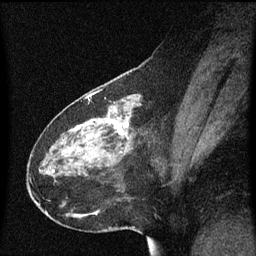
Breast MRI (dynamic contrast-enhanced), one sagittal slice; position 25 of 60 along the scan axis; dynamic contrast-enhanced series, image 2 of 3 at this slice position (ordered by acquisition); 1.5 T; TE 4.2 ms, TR 8.4 ms; 2 mm slice thickness; 256 × 256 image matrix. Patient: female, 49 years. From the clinical record (not read from this slice): setting: breast cancer imaged before/during neoadjuvant chemotherapy; receptor status: HR-positive, HER2-negative.
Structures marked on this image (semi-automatically segmented with operator editing):
- analysis volume of interest (the breast-tissue region the enhancement analysis was run in; not a lesion): bounding box [x1, y1, x2, y2] px = [28, 96, 164, 221]
- tumour enhancement mask (voxels above the 70 % enhancement threshold inside the analysis volume of interest): [113, 122, 129, 135]